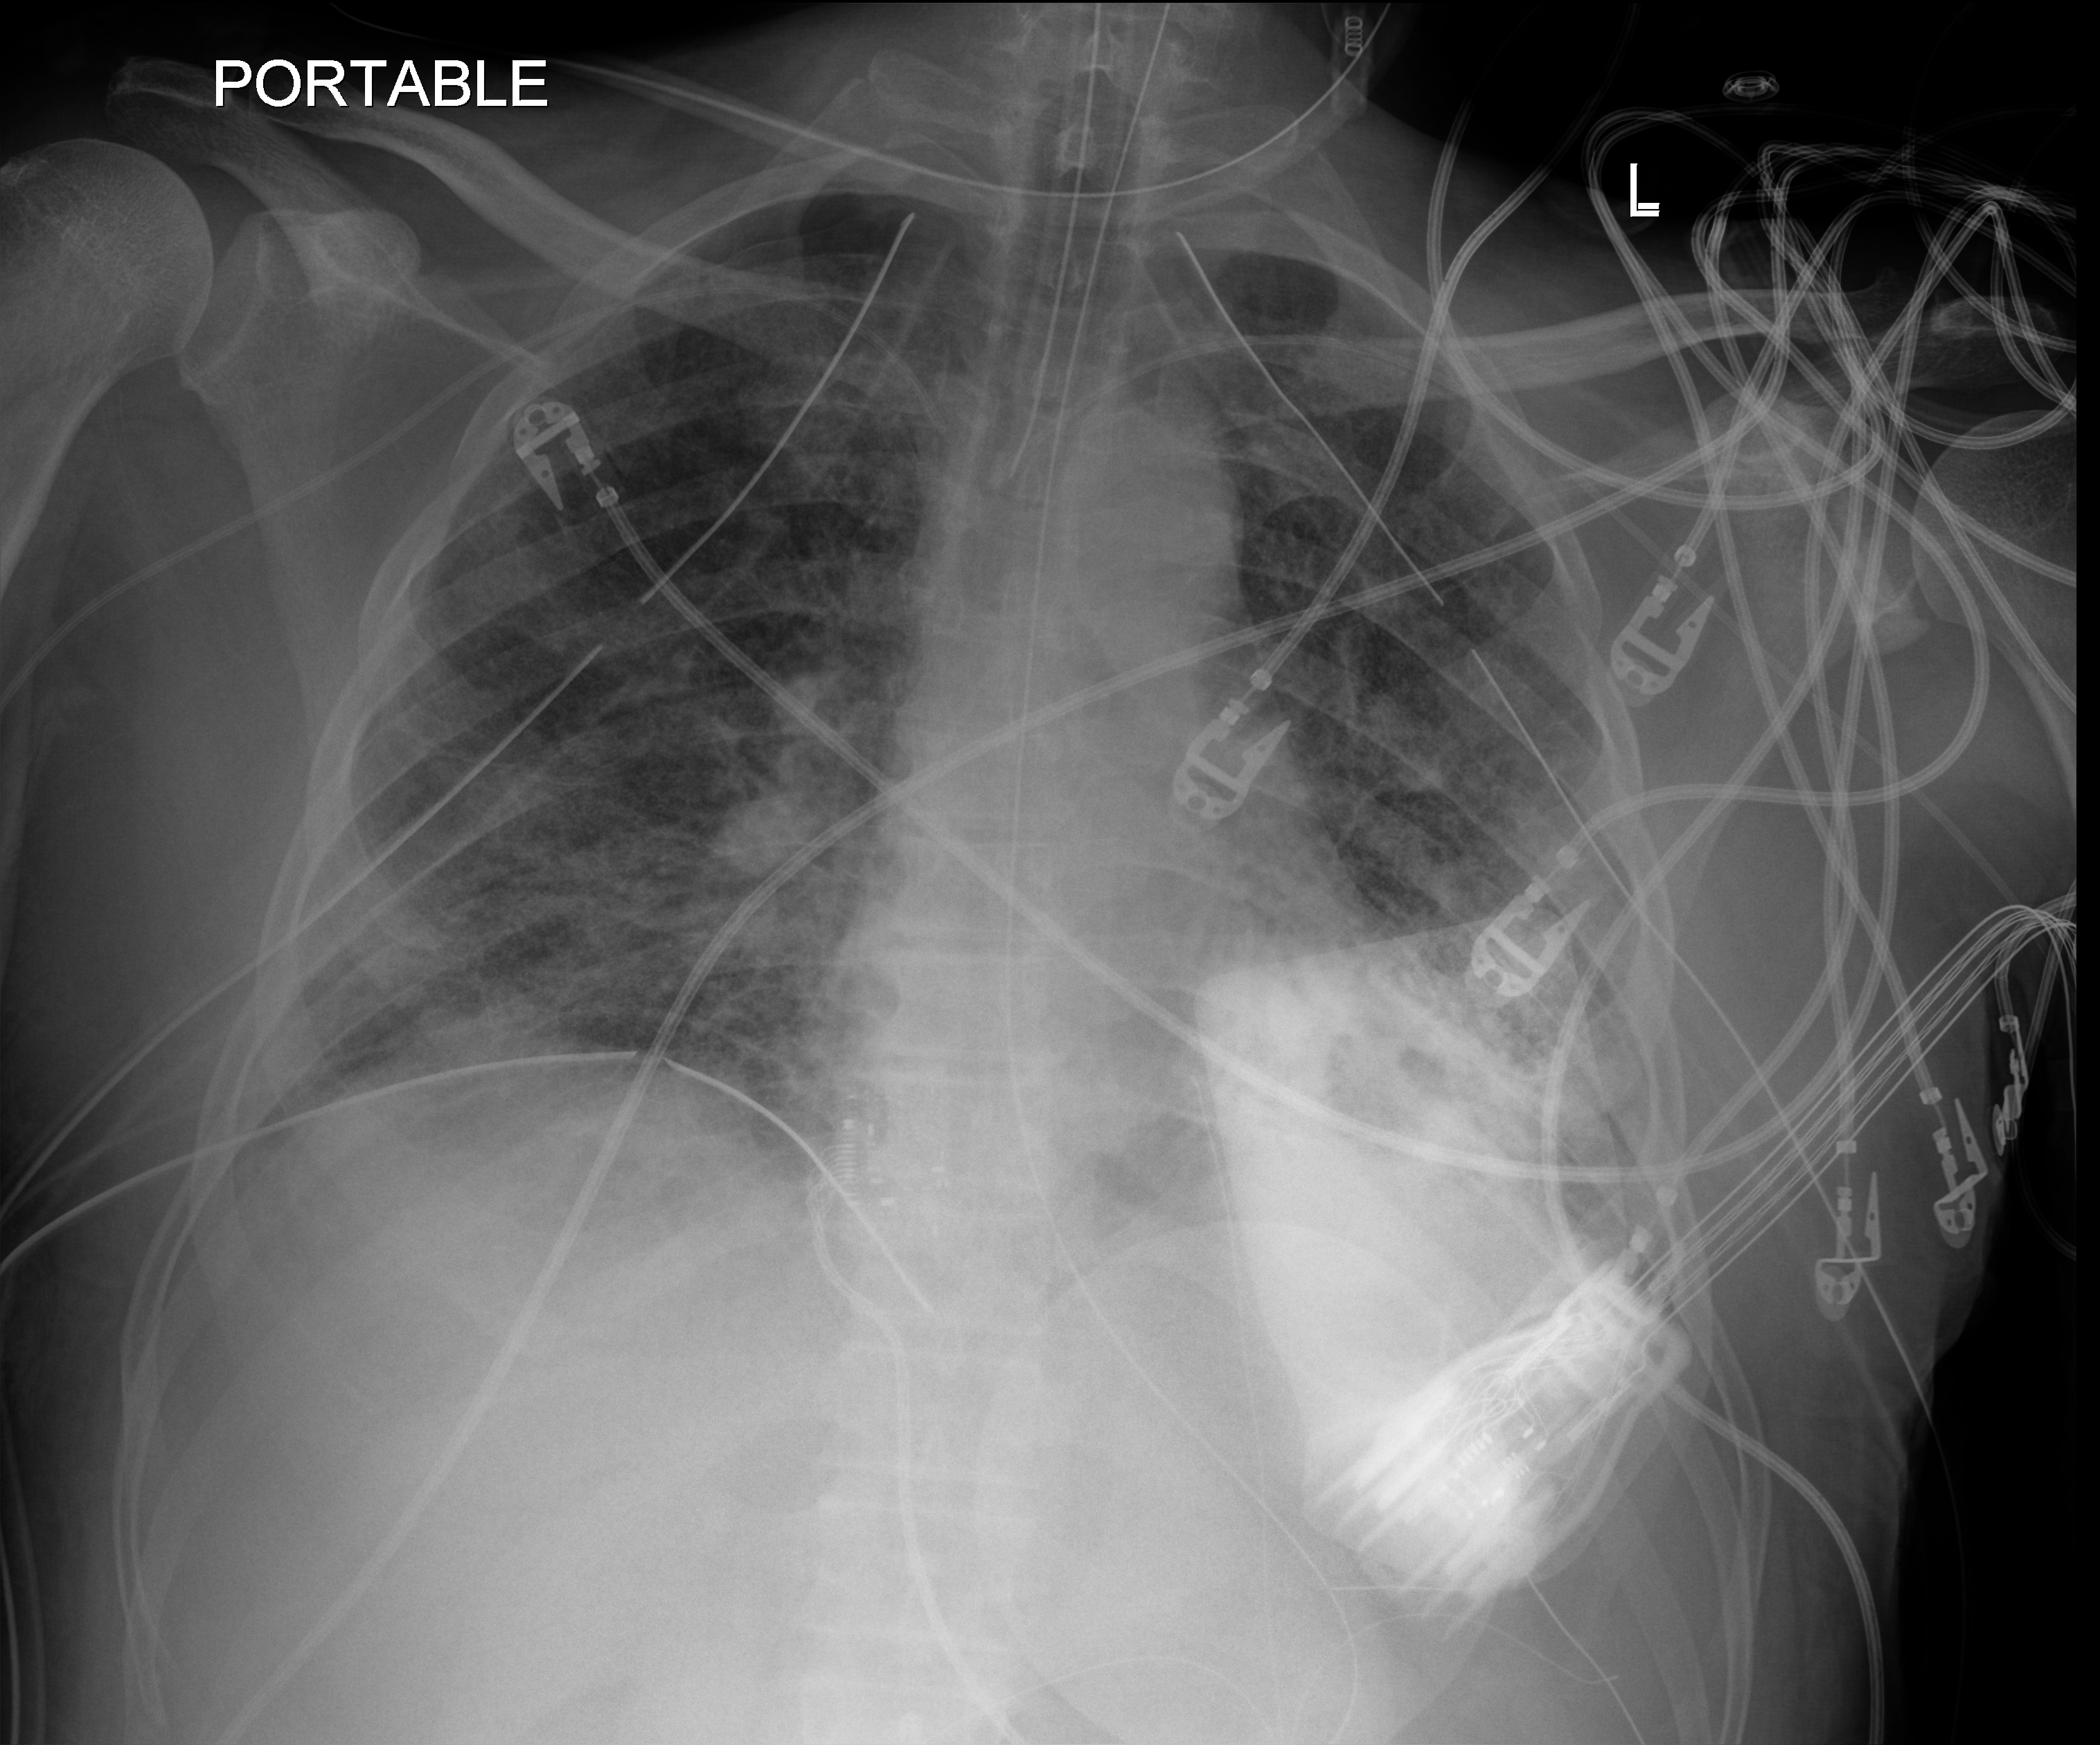
Bedside chest radiograph (digital radiography), anteroposterior (AP) projection. Male patient hospitalised with COVID-19, age 18–59 years.
Admission-level facts for this patient (not findings on this image; timing relative to this image not recorded):
- smoking status (admission record): never
- mechanically ventilated during this hospital stay: yes